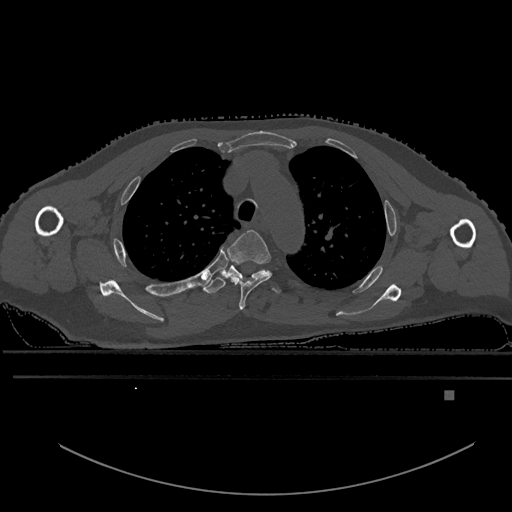
CT including the spine, one axial slice; slice 433 of 969 in the series (ordered by position); bone window (W 1800 / L 400 HU); 0.5 mm slice thickness; 512 × 512 image matrix, field of view 456 × 456 mm. Patient: male, 82 years. From the clinical record (not read from this slice): primary cancer: prostate; vertebrae with lytic lesions (as recorded): T11, T9, T8, T2.
Structures marked on this image (semi-automatically segmented with operator editing):
- T3 vertebra: bounding box [x1, y1, x2, y2] px = [227, 230, 272, 310]
- T4 vertebra: [203, 263, 282, 294]